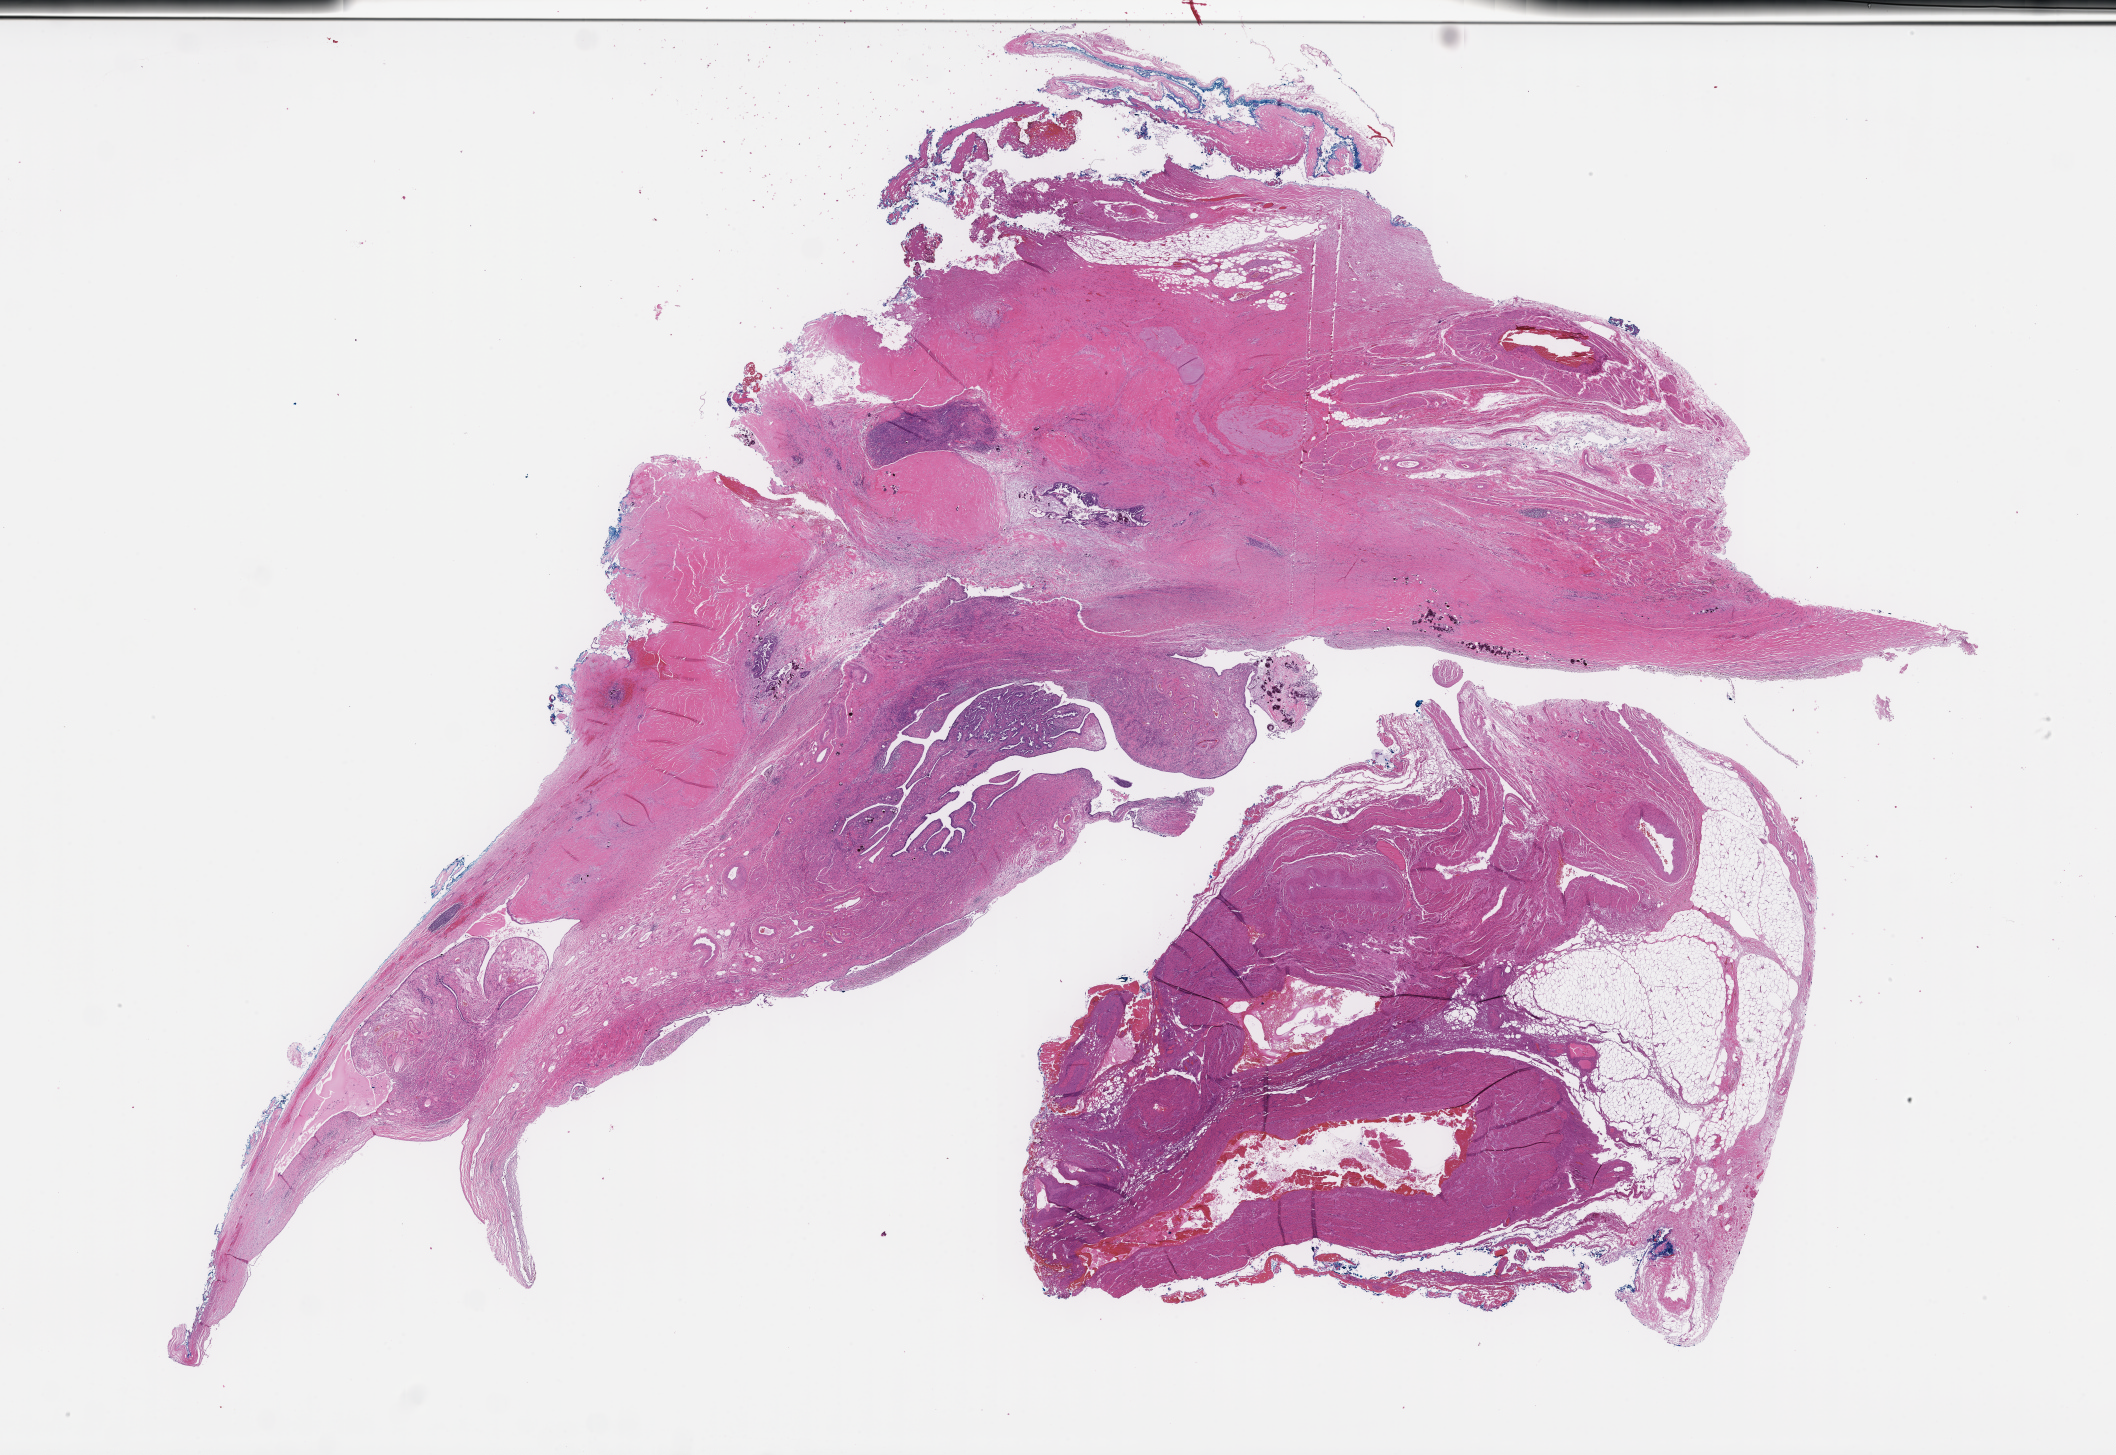
Digitized hematoxylin and eosin (H&E)-stained section — whole scanned area (about 34.2 x 23.5 mm) shown as a low-resolution overview. FFPE section. Site: ovary. Archival tissue. Patient: female.
This section: primary tumour tissue. Diagnosis: Ovarian Carcinoma.